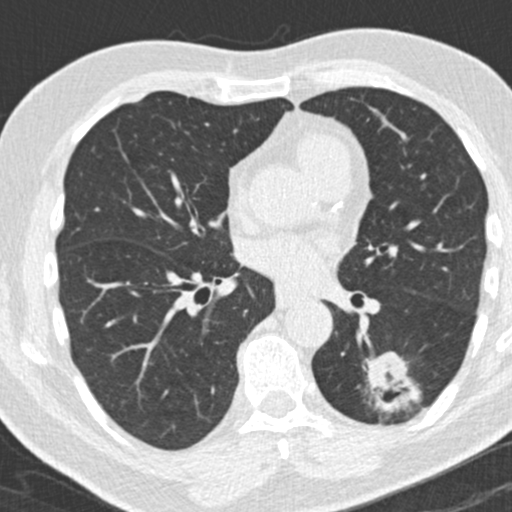
Low-dose screening chest CT, axial slice, third annual screen, lung window (W 1500 / L -600 HU), standard (soft-tissue) reconstruction kernel (B30f), 120 kVp, slice 85 of 180 in the series. Male participant, aged 66 years at enrolment.
Lesion marked by an expert reader, bounding box (x1, y1, x2, y2) in pixels: (356, 352, 425, 428). Reader record for this screening exam (exam-level; its link to the box is not recorded): non-calcified nodule or mass ≥4 mm, left lower lobe, 31 × 24 mm, spiculated (stellate) margins, pre-existing on the prior screen: yes; interval growth: yes. Official screen result: positive, other. Lung cancer was diagnosed 56 days after this screen: adenocarcinoma, NOS, left lower lobe, poorly differentiated (G3), stage IB (AJCC 6th edition), 38 mm at pathology.